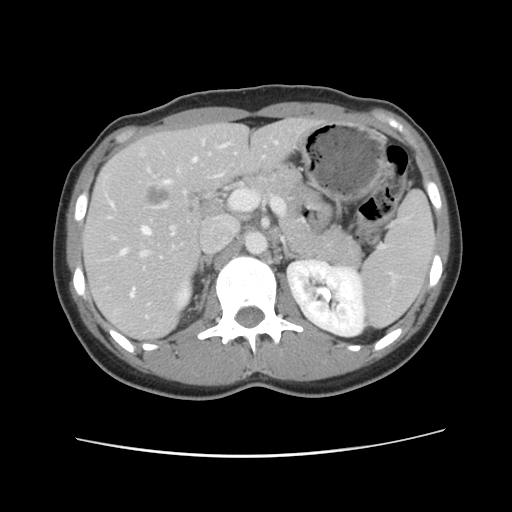
Contrast-enhanced abdominal CT, one axial slice. Slice 60 of 134 in the series (ordered by position). Intravenous contrast given. Soft-tissue window (W 400 / L 40 HU). 2.5 mm slice thickness. 512 × 512 image matrix, field of view 339 × 339 mm. Female patient, age 33 years. Case-level facts recorded for this patient, not image findings: diagnosis: colorectal cancer liver metastases, imaged before liver resection.
Structures marked on this image (expert manual segmentation):
- hepatic veins: bounding box <112,142,277,297> (left, top, right, bottom; pixels)
- liver: <85,119,317,339>
- planned liver remnant (the part of the liver to remain after resection): <85,119,317,339>
- portal vein (with intrahepatic branches): <138,225,177,269>
- liver metastasis: <143,182,173,209>